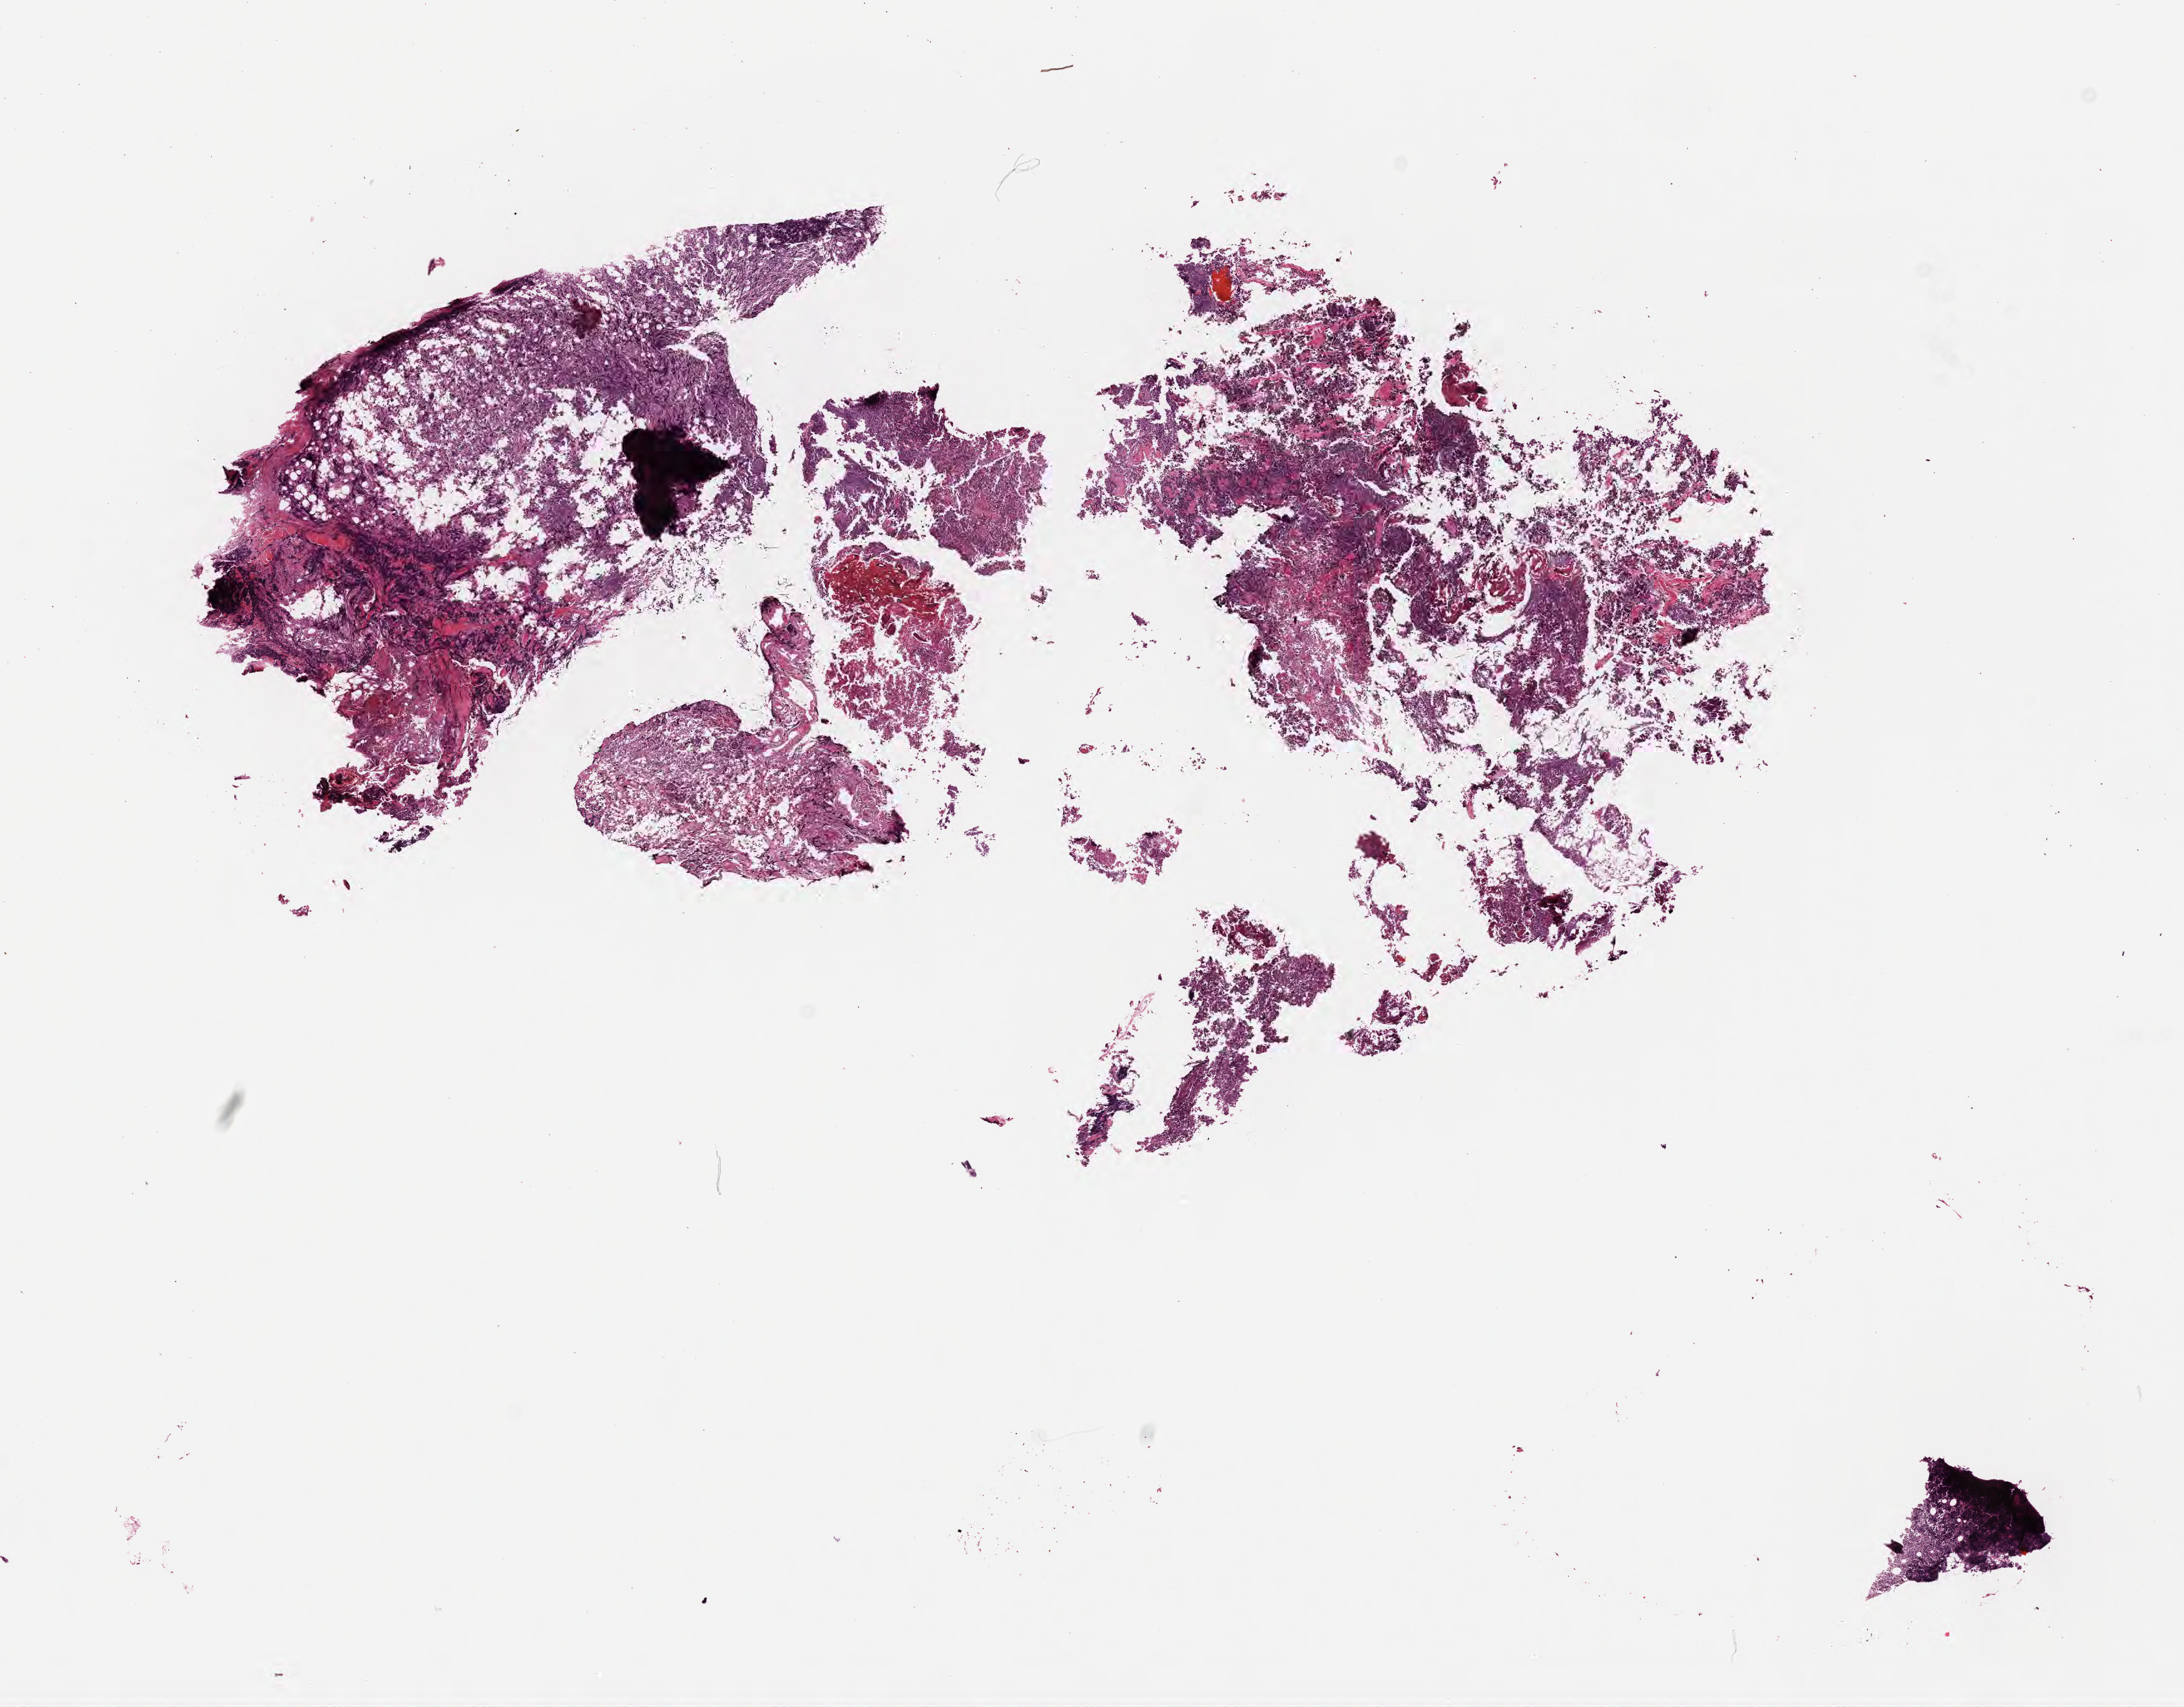
Digitized H&E-stained section — whole scanned area (about 14.1 x 11.0 mm) shown as a low-resolution overview; formalin-fixed paraffin-embedded section; specimen: primary tumor. Patient male; 23 years old.
Diagnosis: Burkitt lymphoma, NOS.